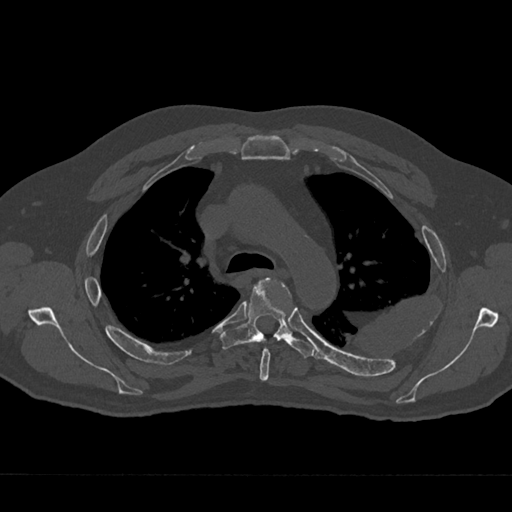
CT including the spine, one axial slice; slice 491 of 797 in the series (ordered by position); reconstruction kernel Br40s/3; 120 kVp; bone window (W 1800 / L 400 HU); 0.5 mm slice thickness; 512 × 512 image matrix, field of view 377 × 377 mm. Patient: male, 75 years. From the clinical record (not read from this slice): primary cancer: renal.
Annotated regions visible in this slice (semi-automatically segmented with operator editing):
- T4 vertebra: bounding box [x1, y1, x2, y2] px = [260, 283, 291, 381]
- T5 vertebra: [220, 278, 314, 358]